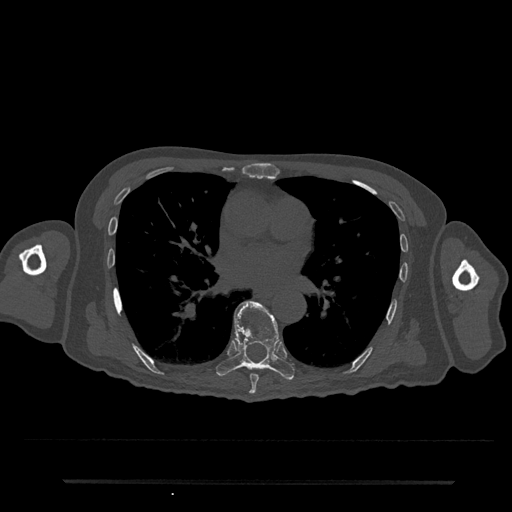
CT including the spine, one axial slice; slice 440 of 797 in the series (ordered by position); reconstruction kernel Br40s/3; 120 kVp; bone window (W 1800 / L 400 HU); 512 × 512 image matrix, field of view 427 × 427 mm. Patient: male, 74 years. From the clinical record (not read from this slice): primary cancer: prostate.
Structures marked on this image (semi-automatic segmentation, software-assisted and operator-edited):
- T7 vertebra: bounding box <249,374,259,394> (left, top, right, bottom; pixels)
- T8 vertebra: <216,301,295,381>